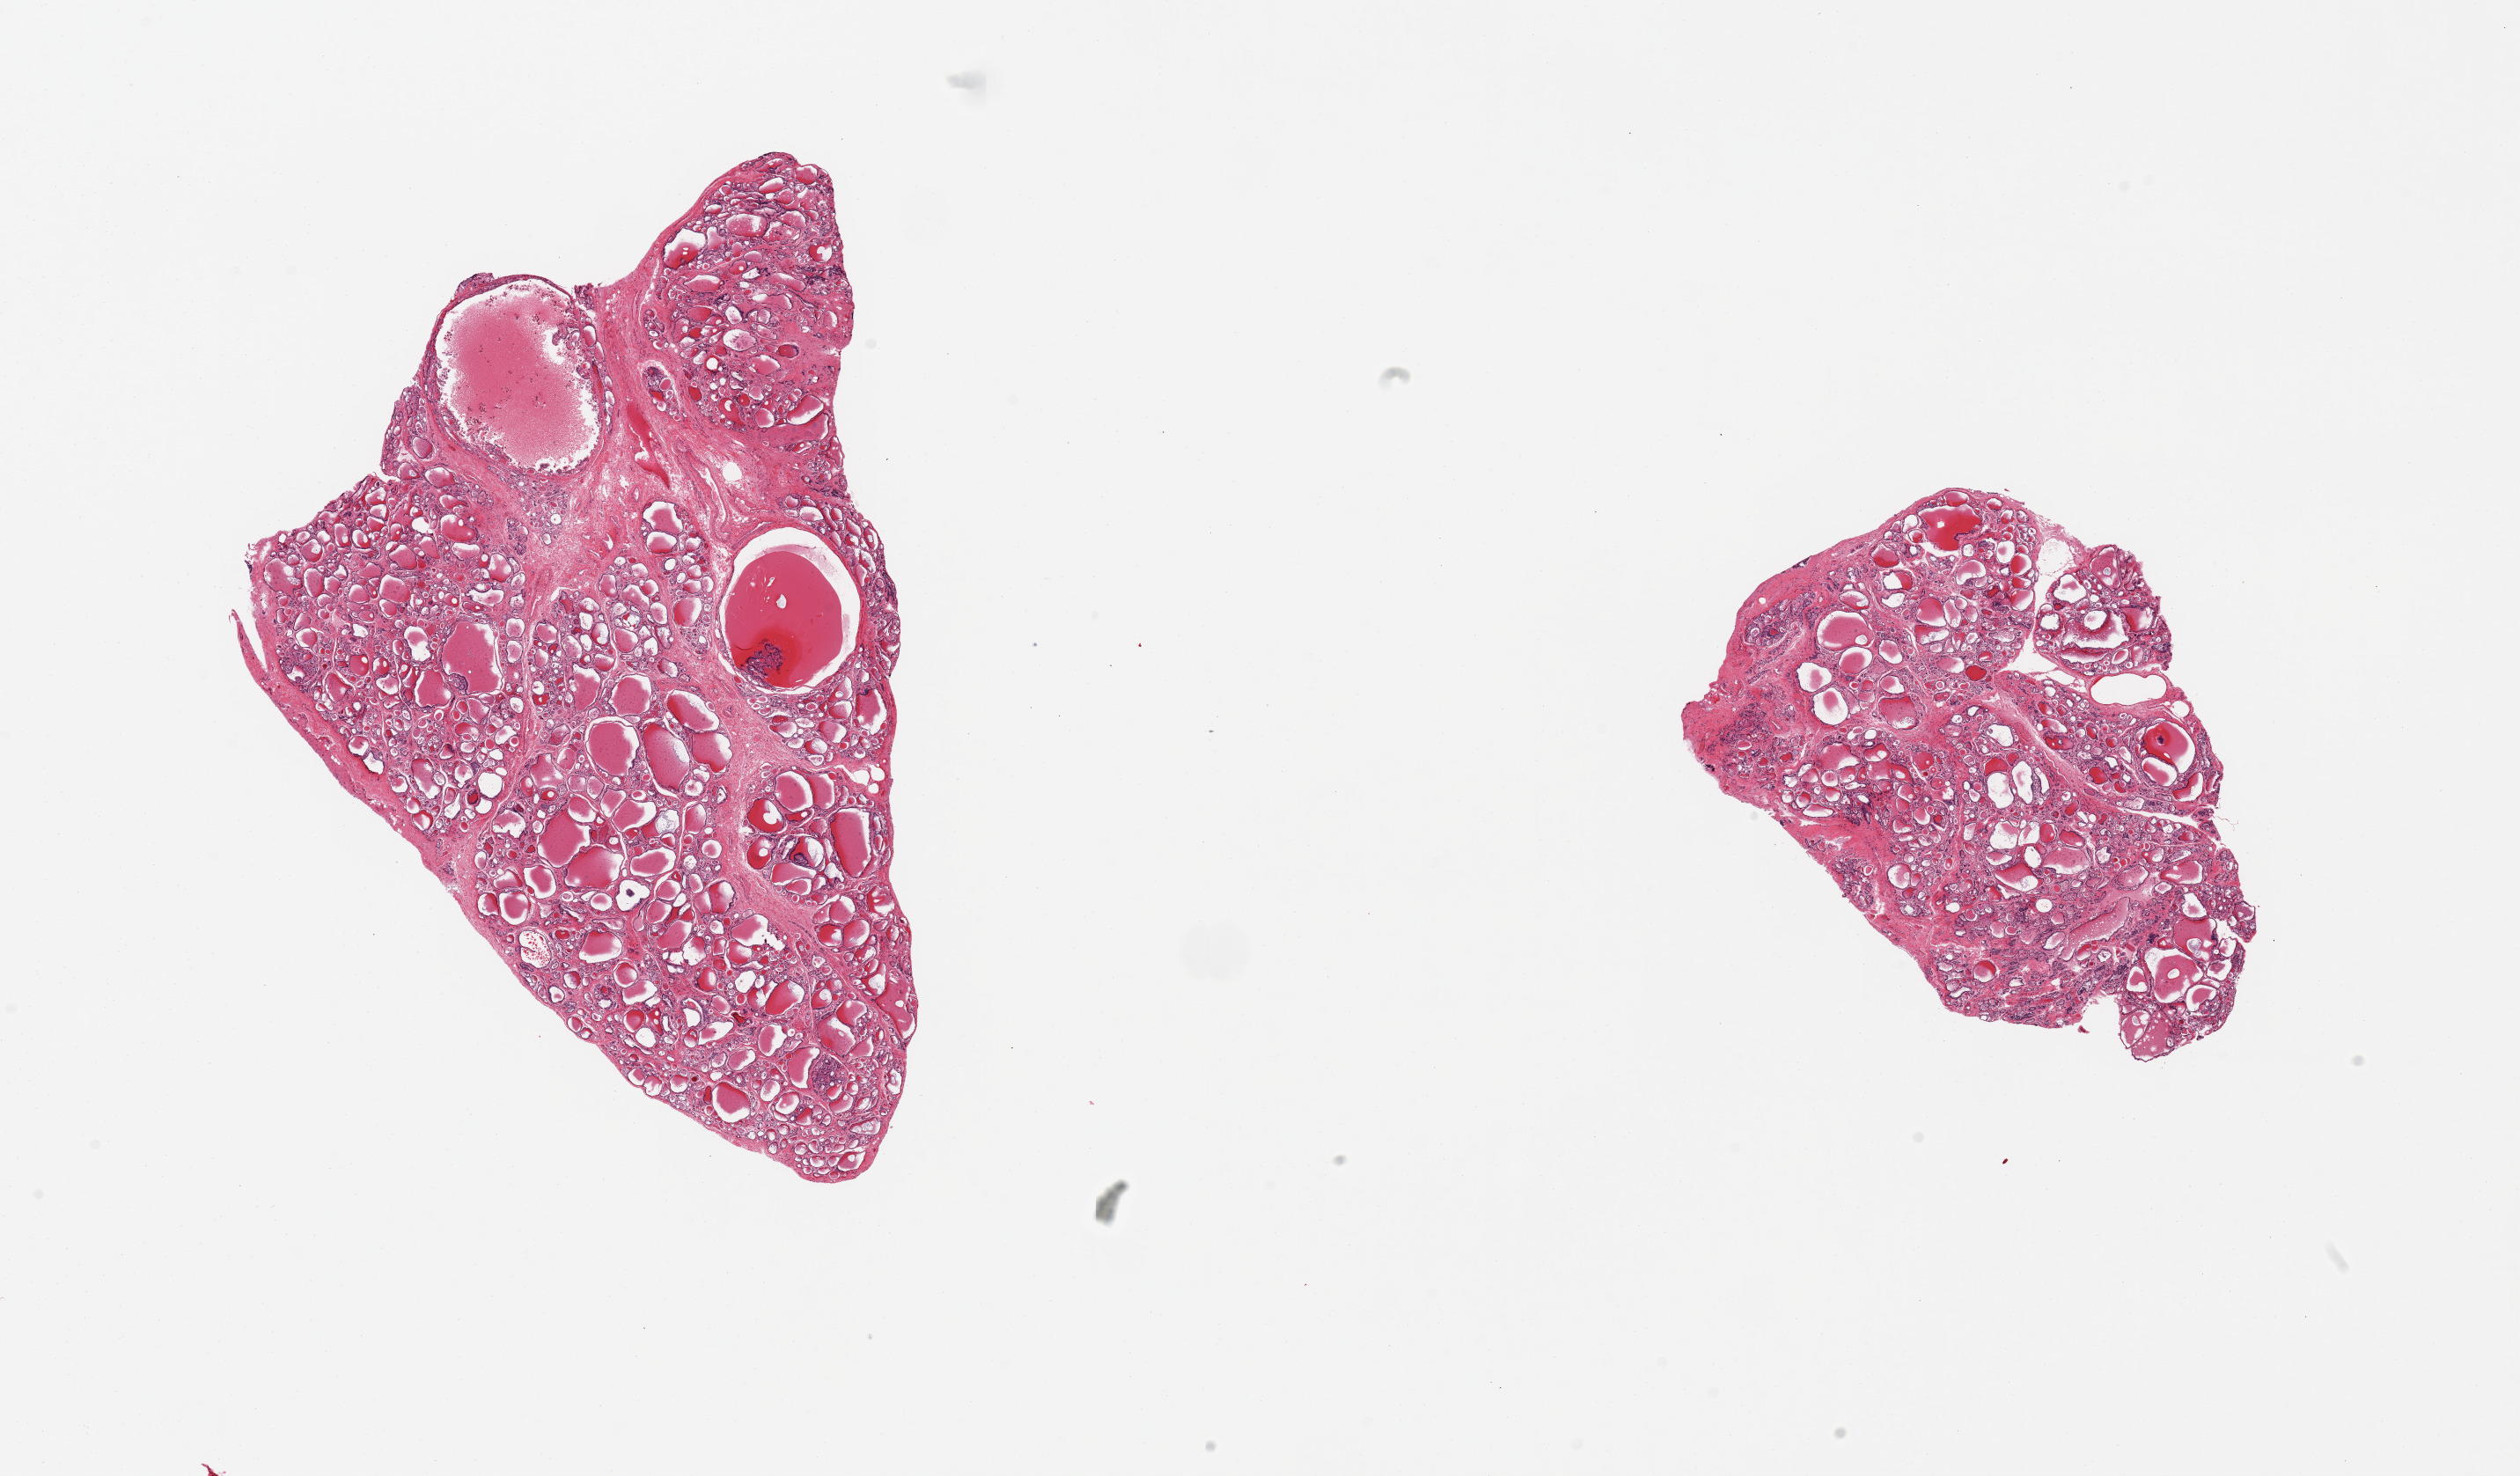
Whole-slide image, H&E stain, a low-resolution overview of the entire scanned area, about 22.6 x 13.3 mm (slide scanned at 20x). PAXgene-fixed paraffin-embedded (PFPE) section. Sampled site (target tissue): thyroid. Donor tissue sample.
• reviewer comment on this tissue sample: 2 pieces, colloid cysts up to ~2mm